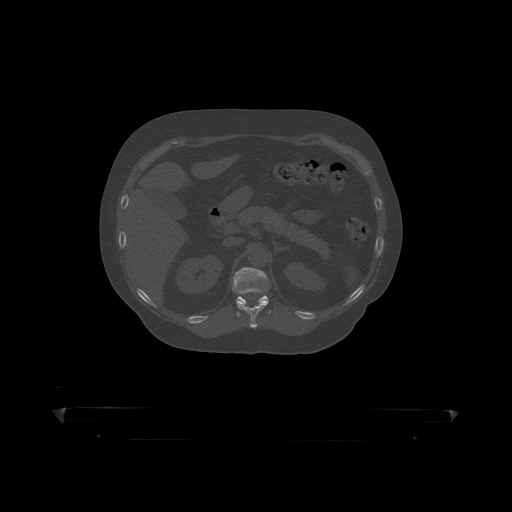
CT including the spine, one axial slice; slice 183 of 390 in the series (ordered by position); bone window (W 1800 / L 400 HU); 1.25 mm slice thickness; 512 × 512 image matrix, field of view 650 × 650 mm. Male patient, age 60 years. Case-level facts recorded for this patient, not image findings: primary cancer: prostate.
Structures marked on this image (semi-automatically segmented with operator editing):
- T11 vertebra: bounding box (x1, y1, x2, y2) in pixels: (237, 288, 268, 319)
- T12 vertebra: (233, 267, 271, 317)